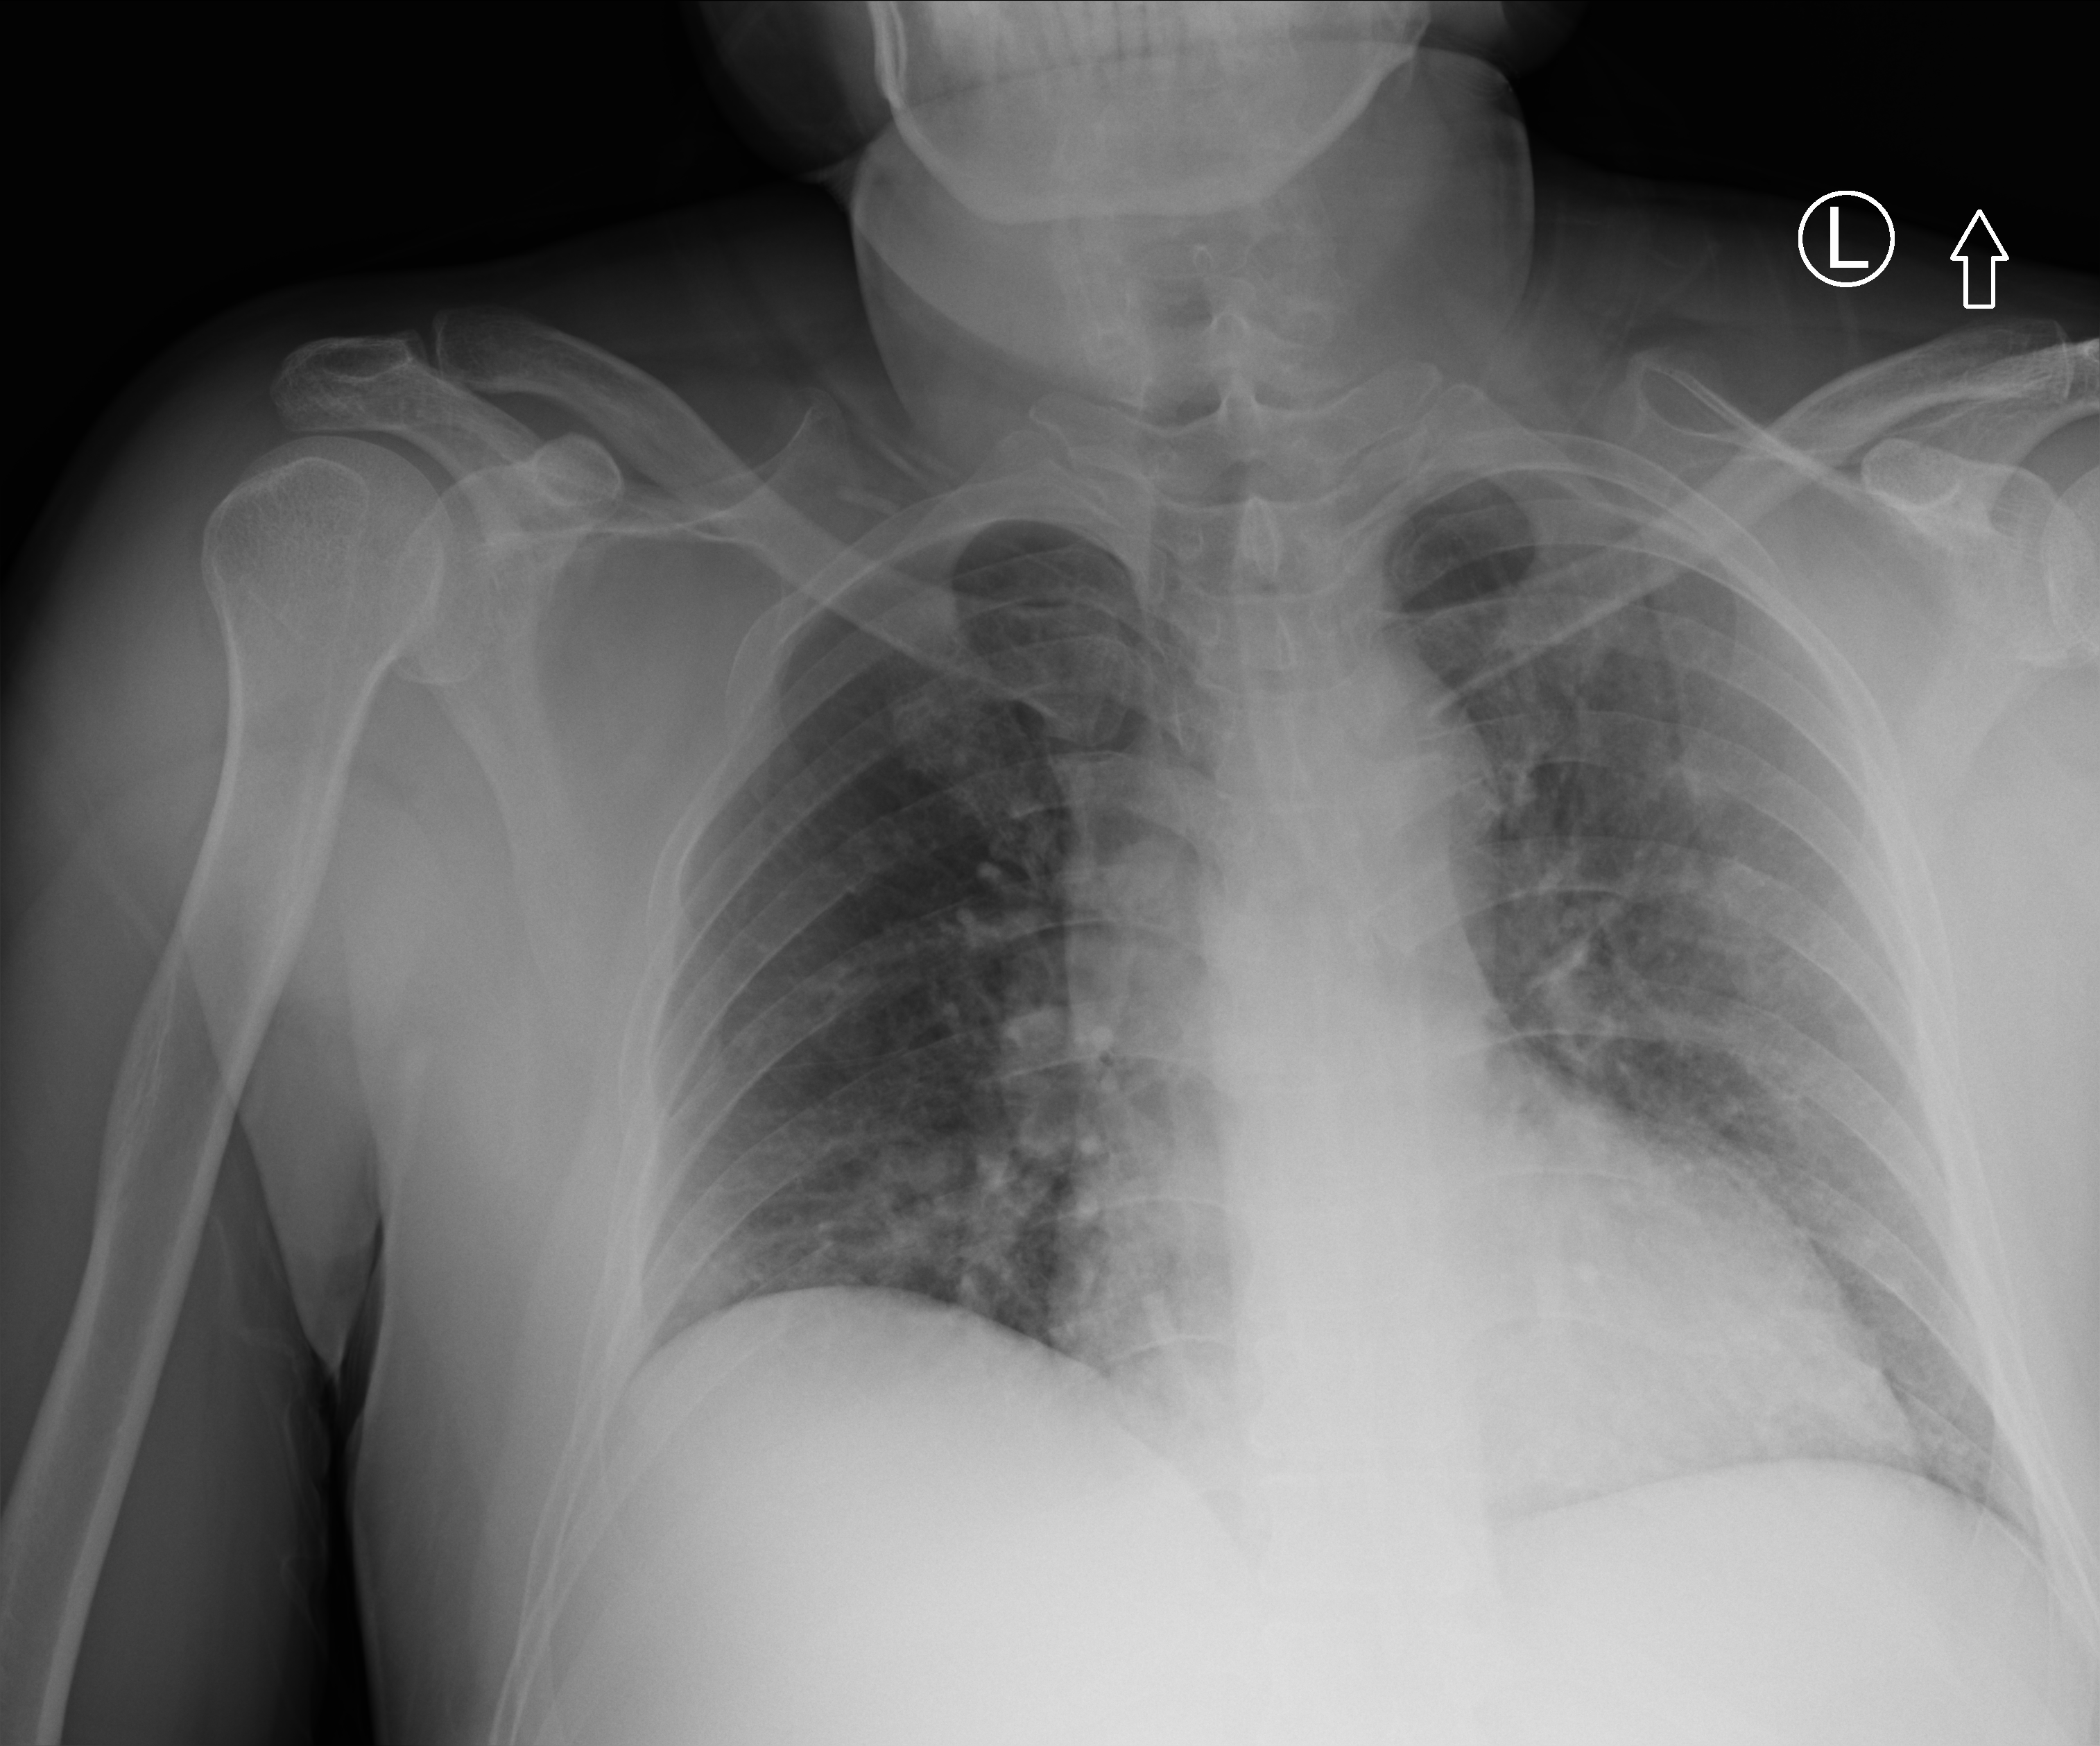
Chest X-ray (portable), anteroposterior (AP) projection. Patient hospitalised with COVID-19; male, aged 18–59 years.
From the hospital-stay record, not from the radiograph (when in the stay this image was taken is not recorded): mechanically ventilated during this hospital stay: no; hypertension (admission record): no; admitted to intensive care during this hospital stay: no.